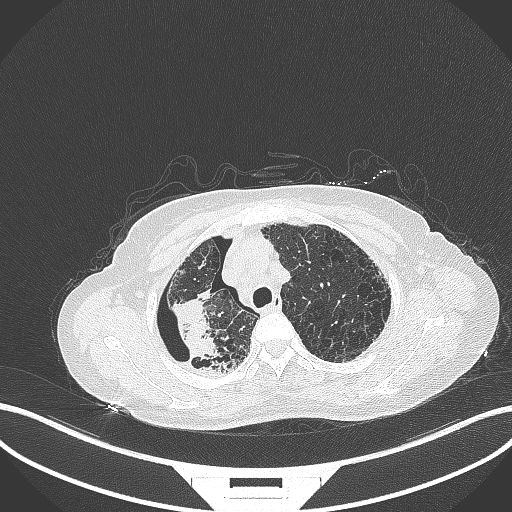
Chest CT, one axial slice; 120 kVp; lung window (W 1500 / L -600 HU); 512 × 512 image matrix, field of view 400 × 400 mm. Female patient, age 64 years. From the clinical record (not read from this slice): clinical TNM (as recorded): T3 N3 M0.
Structures marked on this image (rectangle marked by the reading radiologist):
- lung tumour (recorded histology: squamous cell carcinoma): box from (x=167, y=296) to (x=221, y=368) px